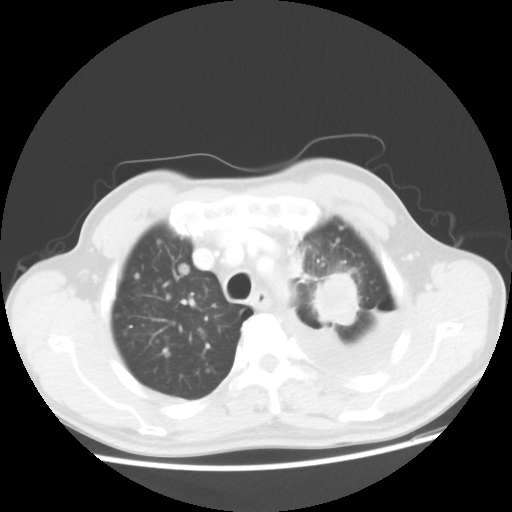
Chest CT, one axial slice. Slice 39 of 48 in the series (ordered by position). Reconstruction kernel STANDARD. Lung window (W 1500 / L -600 HU). 5 mm slice thickness. 512 × 512 image matrix. Patient: male, 55 years. Case-level facts recorded for this patient, not image findings: clinical TNM (as recorded): T2 N3 M1a.
Structures marked on this image (bounding box drawn by a radiologist):
- lung tumour (recorded histology: squamous cell carcinoma): bounding box [x1, y1, x2, y2] px = [300, 259, 358, 346]